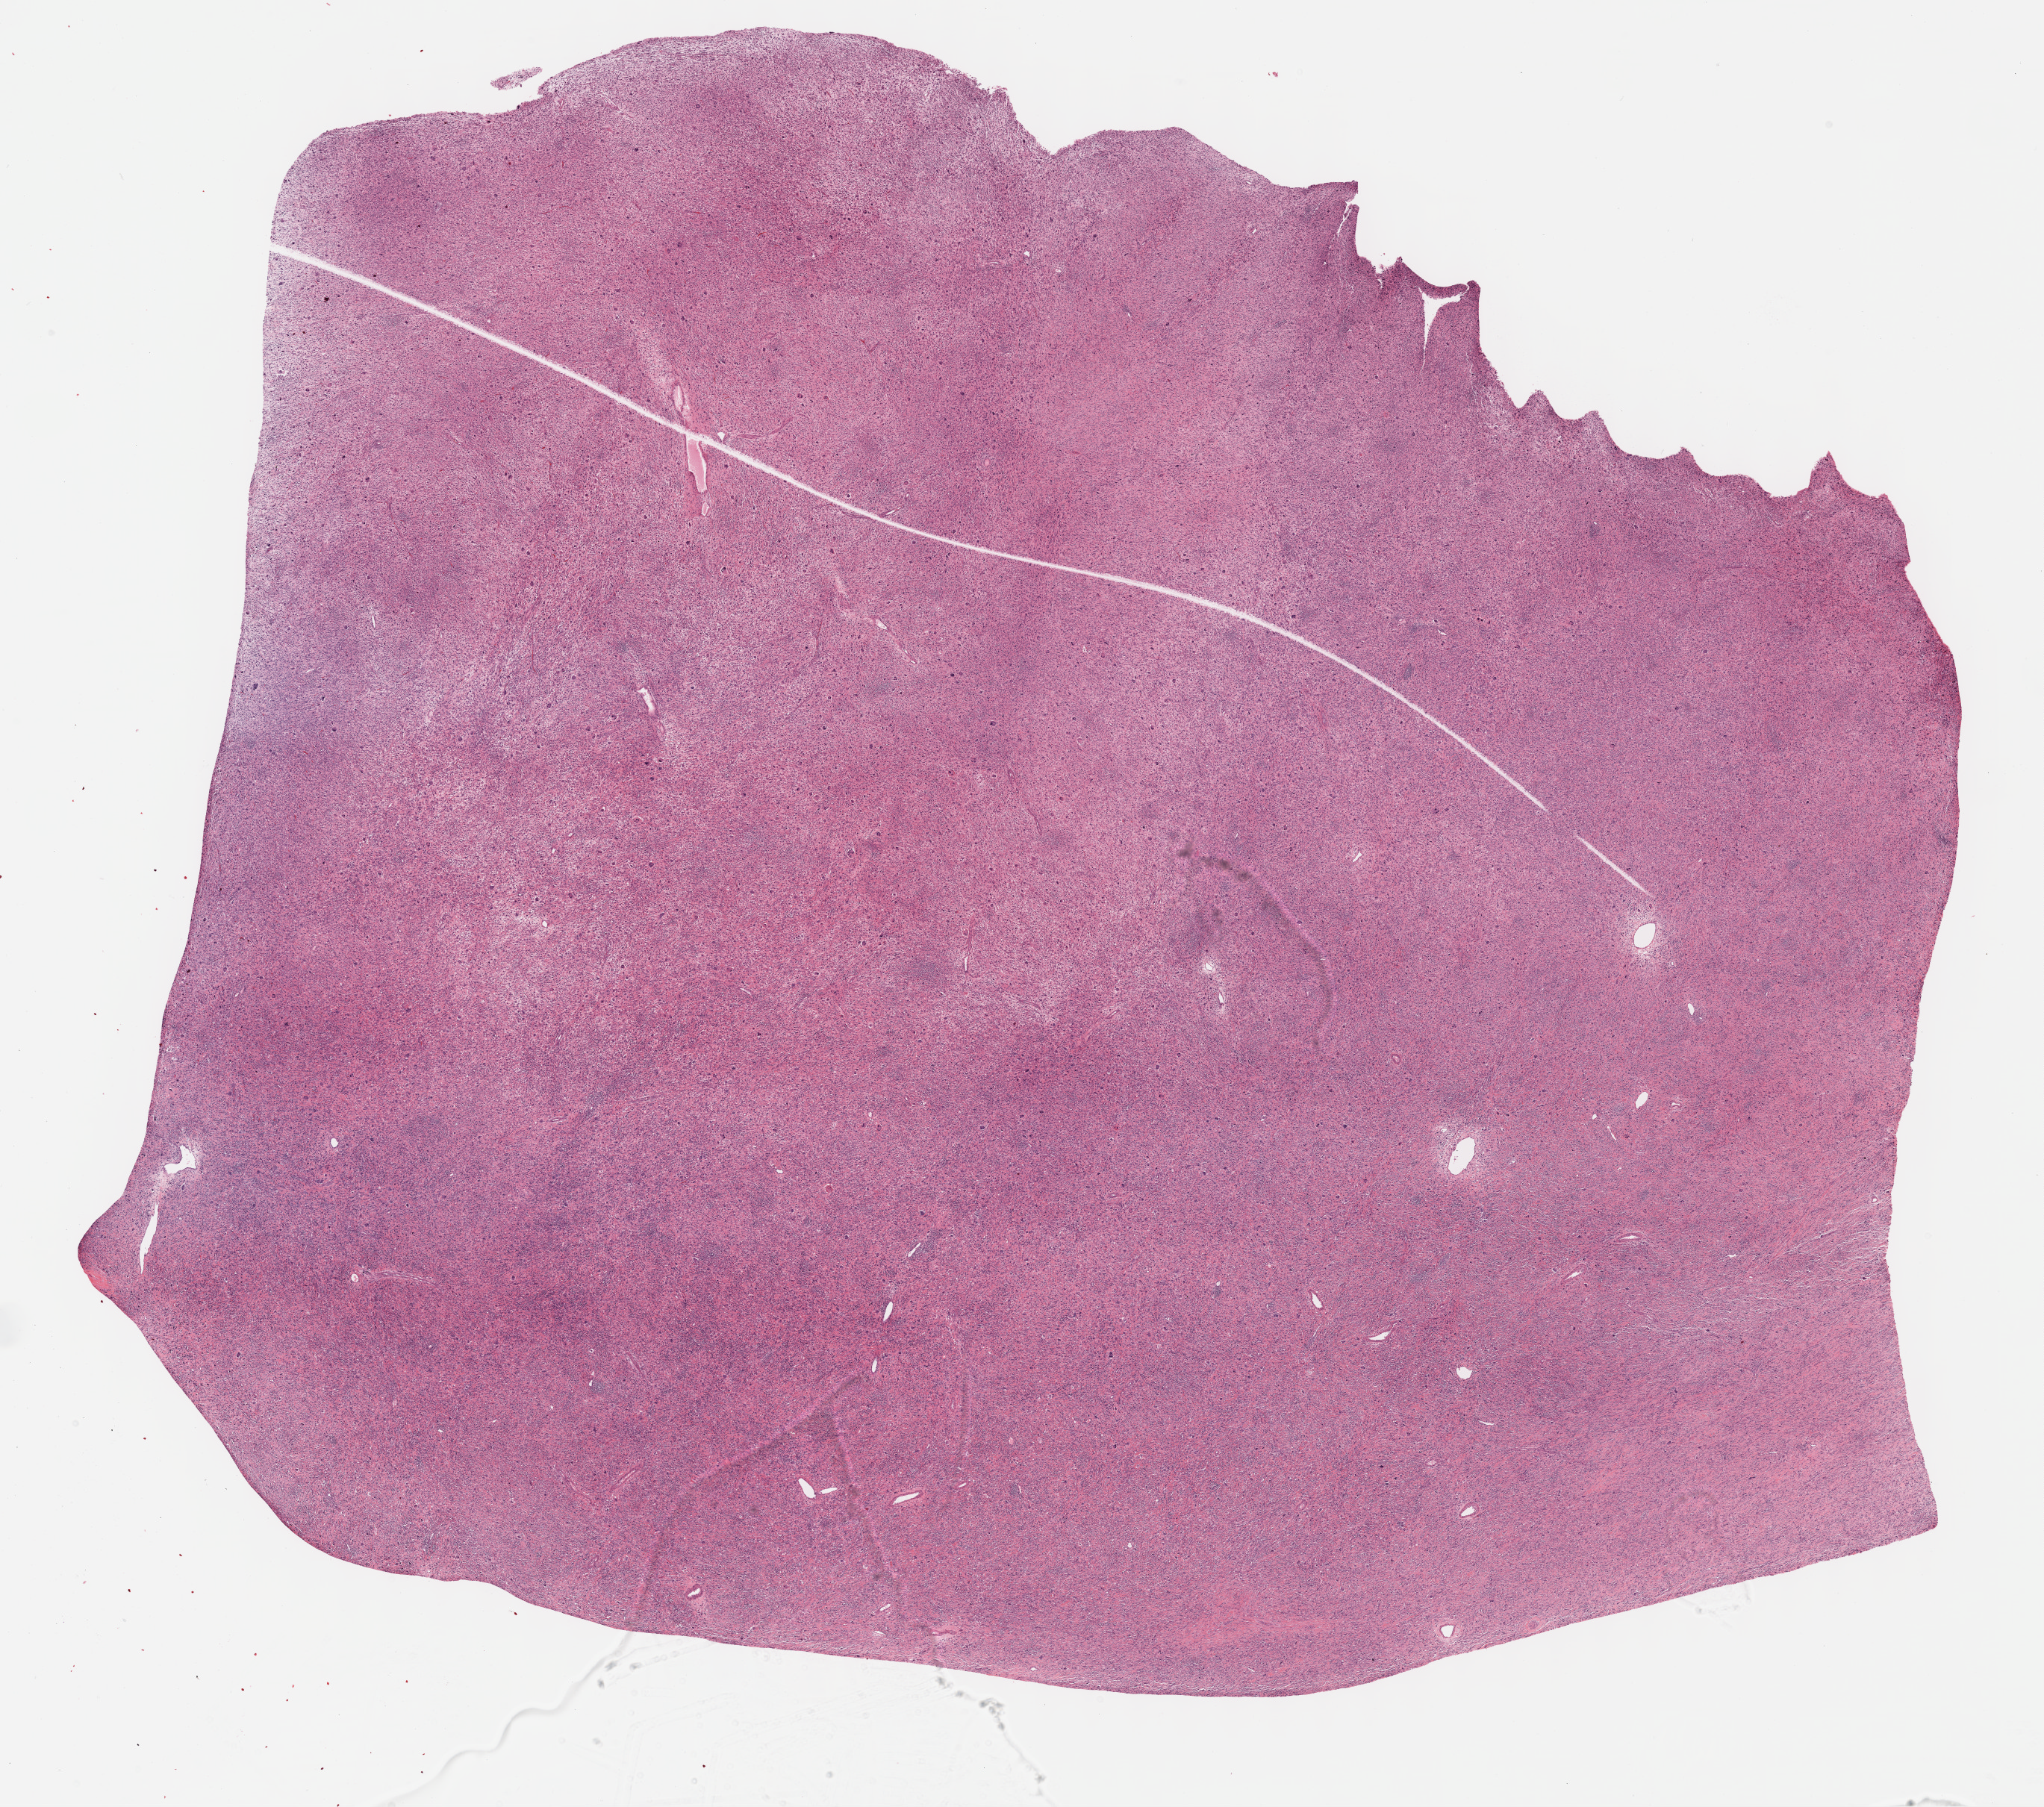
Digitized Hematoxylin and eosin (H&E) stained tissue section (whole slide), whole scanned area (about 22.1 x 19.6 mm, slide scanned at 40x) shown as a low-resolution overview; formalin-fixed paraffin-embedded (FFPE) diagnostic section; primary tumour sample from the retroperitoneum and peritoneum. Patient: male, age at initial diagnosis 60 years.
- histologic diagnosis: Dedifferentiated liposarcoma